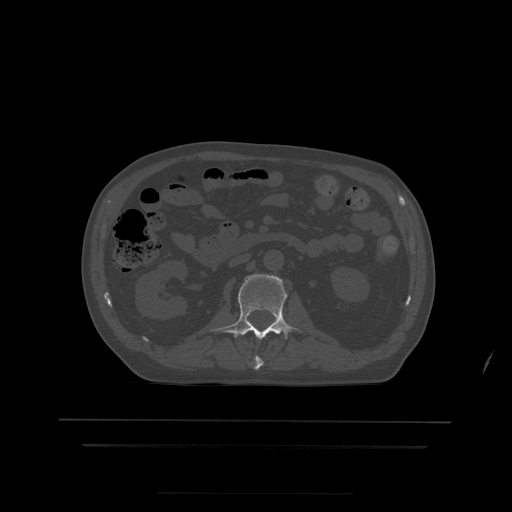
CT including the spine, one axial slice; position 146 of 522 along the scan axis; bone window (W 1800 / L 400 HU); 1.25 mm slice thickness; 512 × 512 image matrix, field of view 436 × 436 mm. Patient age 68 years. Case-level facts recorded for this patient, not image findings: primary cancer: urothelial.
Structures marked on this image (semi-automatically segmented with operator editing):
- L1 vertebra: bounding box [x1, y1, x2, y2] px = [254, 357, 264, 370]
- L2 vertebra: [211, 275, 300, 339]